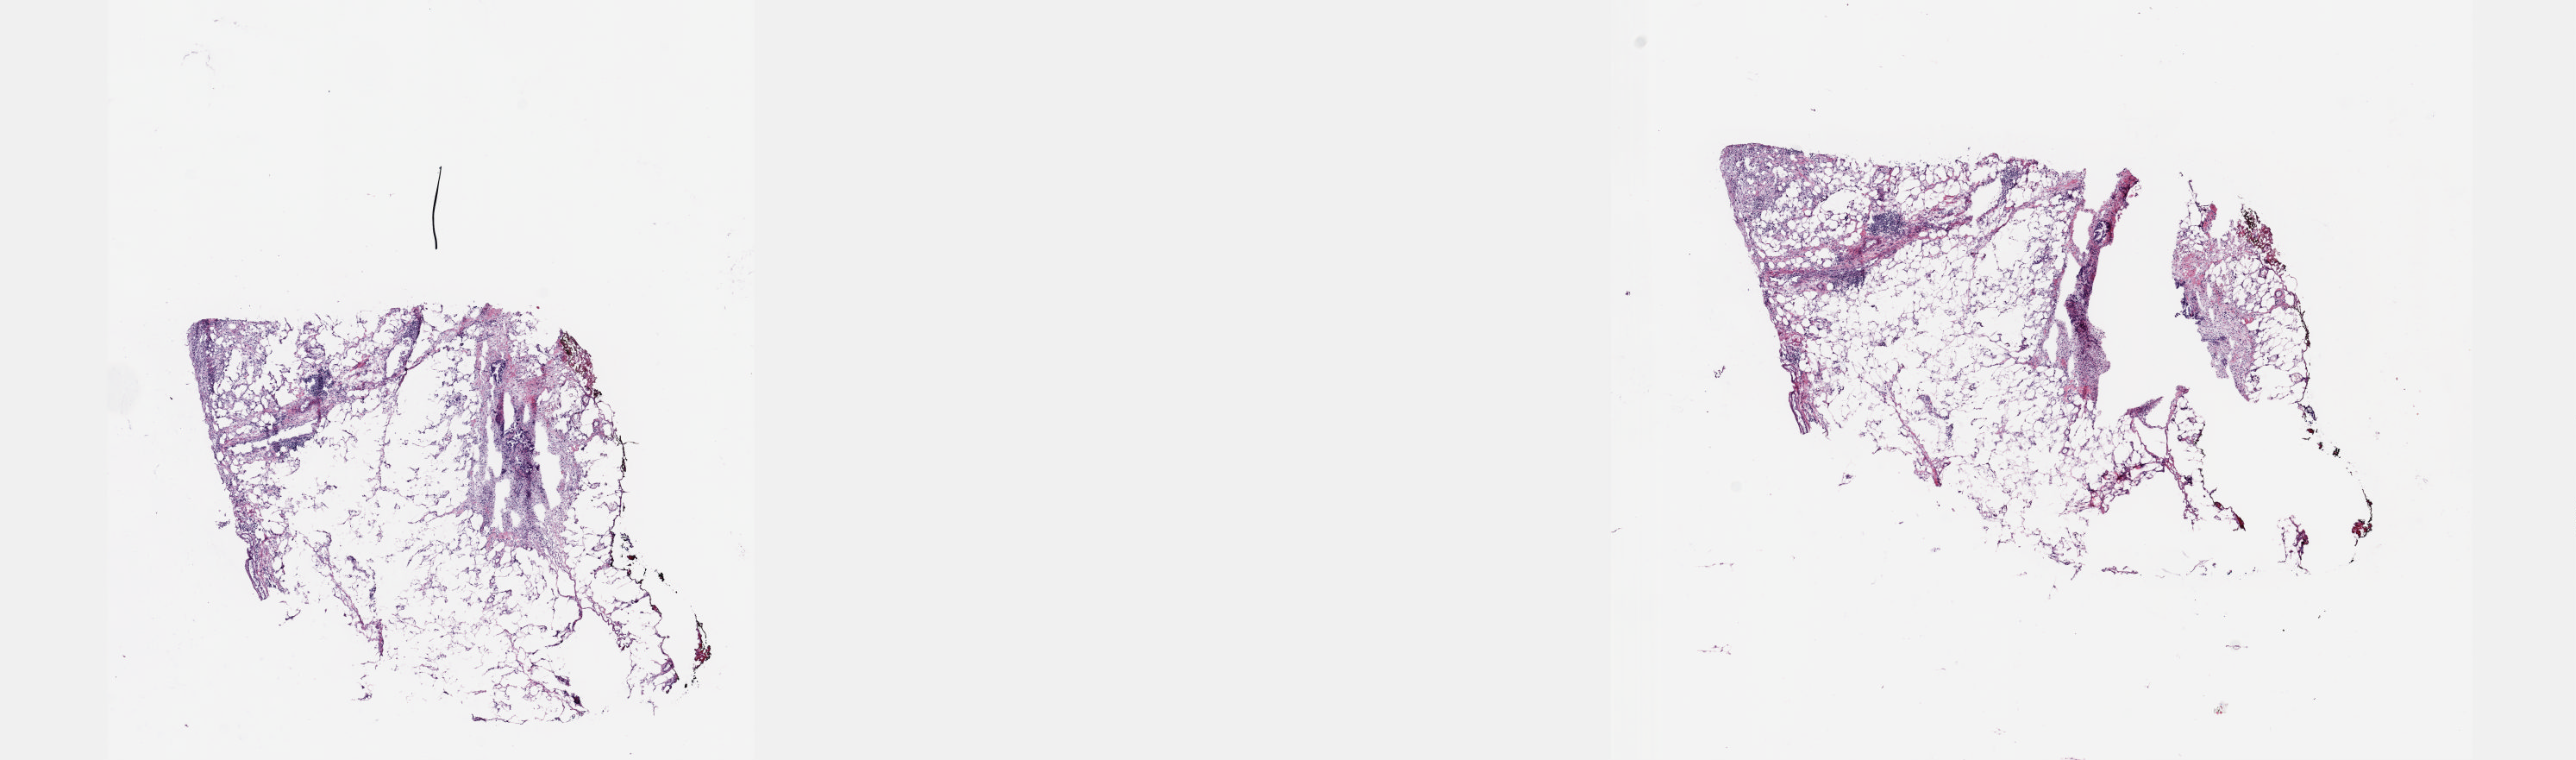
Digitized Hematoxylin and eosin (H&E) stained tissue section (whole slide), shown as a low-resolution overview of the whole scanned area (about 24.1 x 7.1 mm, slide scanned at 20x); frozen section from the top of the tissue portion; sample: solid tissue normal (non-tumour tissue), pancreas. Male, age 59 years at initial diagnosis.
This section: solid tissue normal sample (biorepository sample class). Patient diagnosis: Infiltrating duct carcinoma, NOS (body of pancreas).